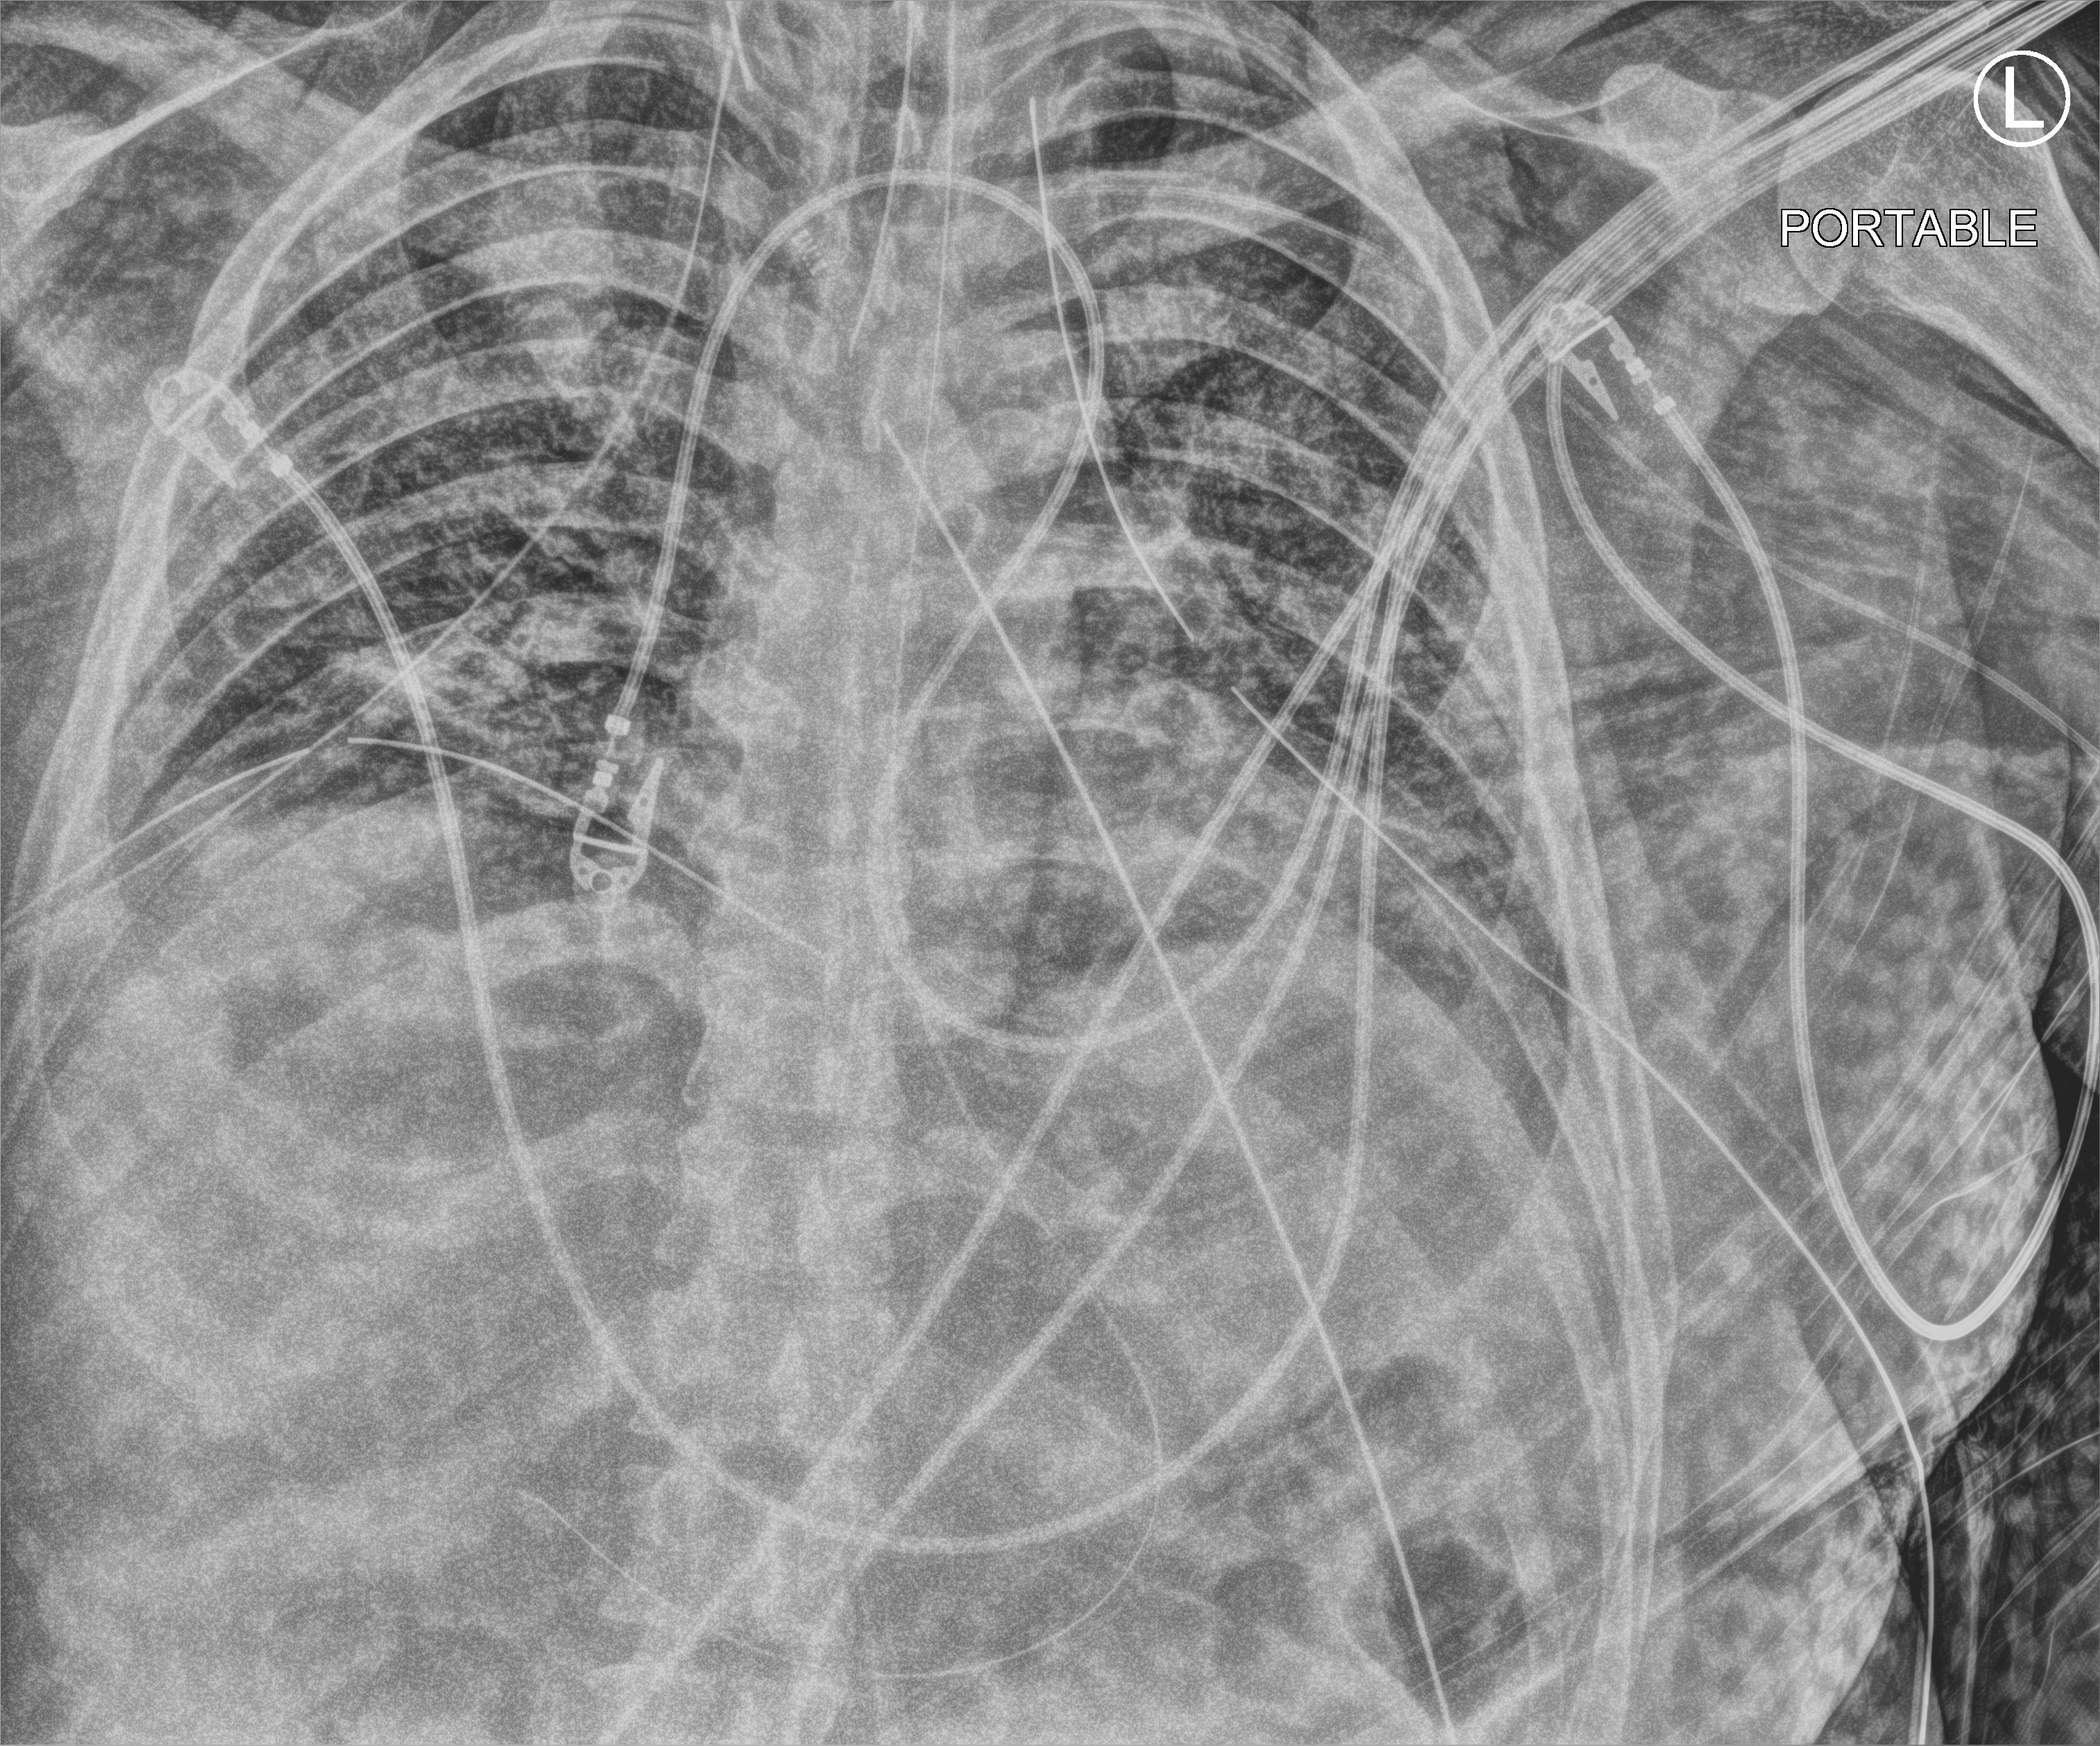
Portable chest radiograph, anteroposterior (AP) projection. Patient hospitalised with COVID-19; male, aged 18–59 years.
Admission-level facts for this patient (not findings on this image; timing relative to this image not recorded): mechanically ventilated during this hospital stay: yes; length of hospital stay: 29 days.